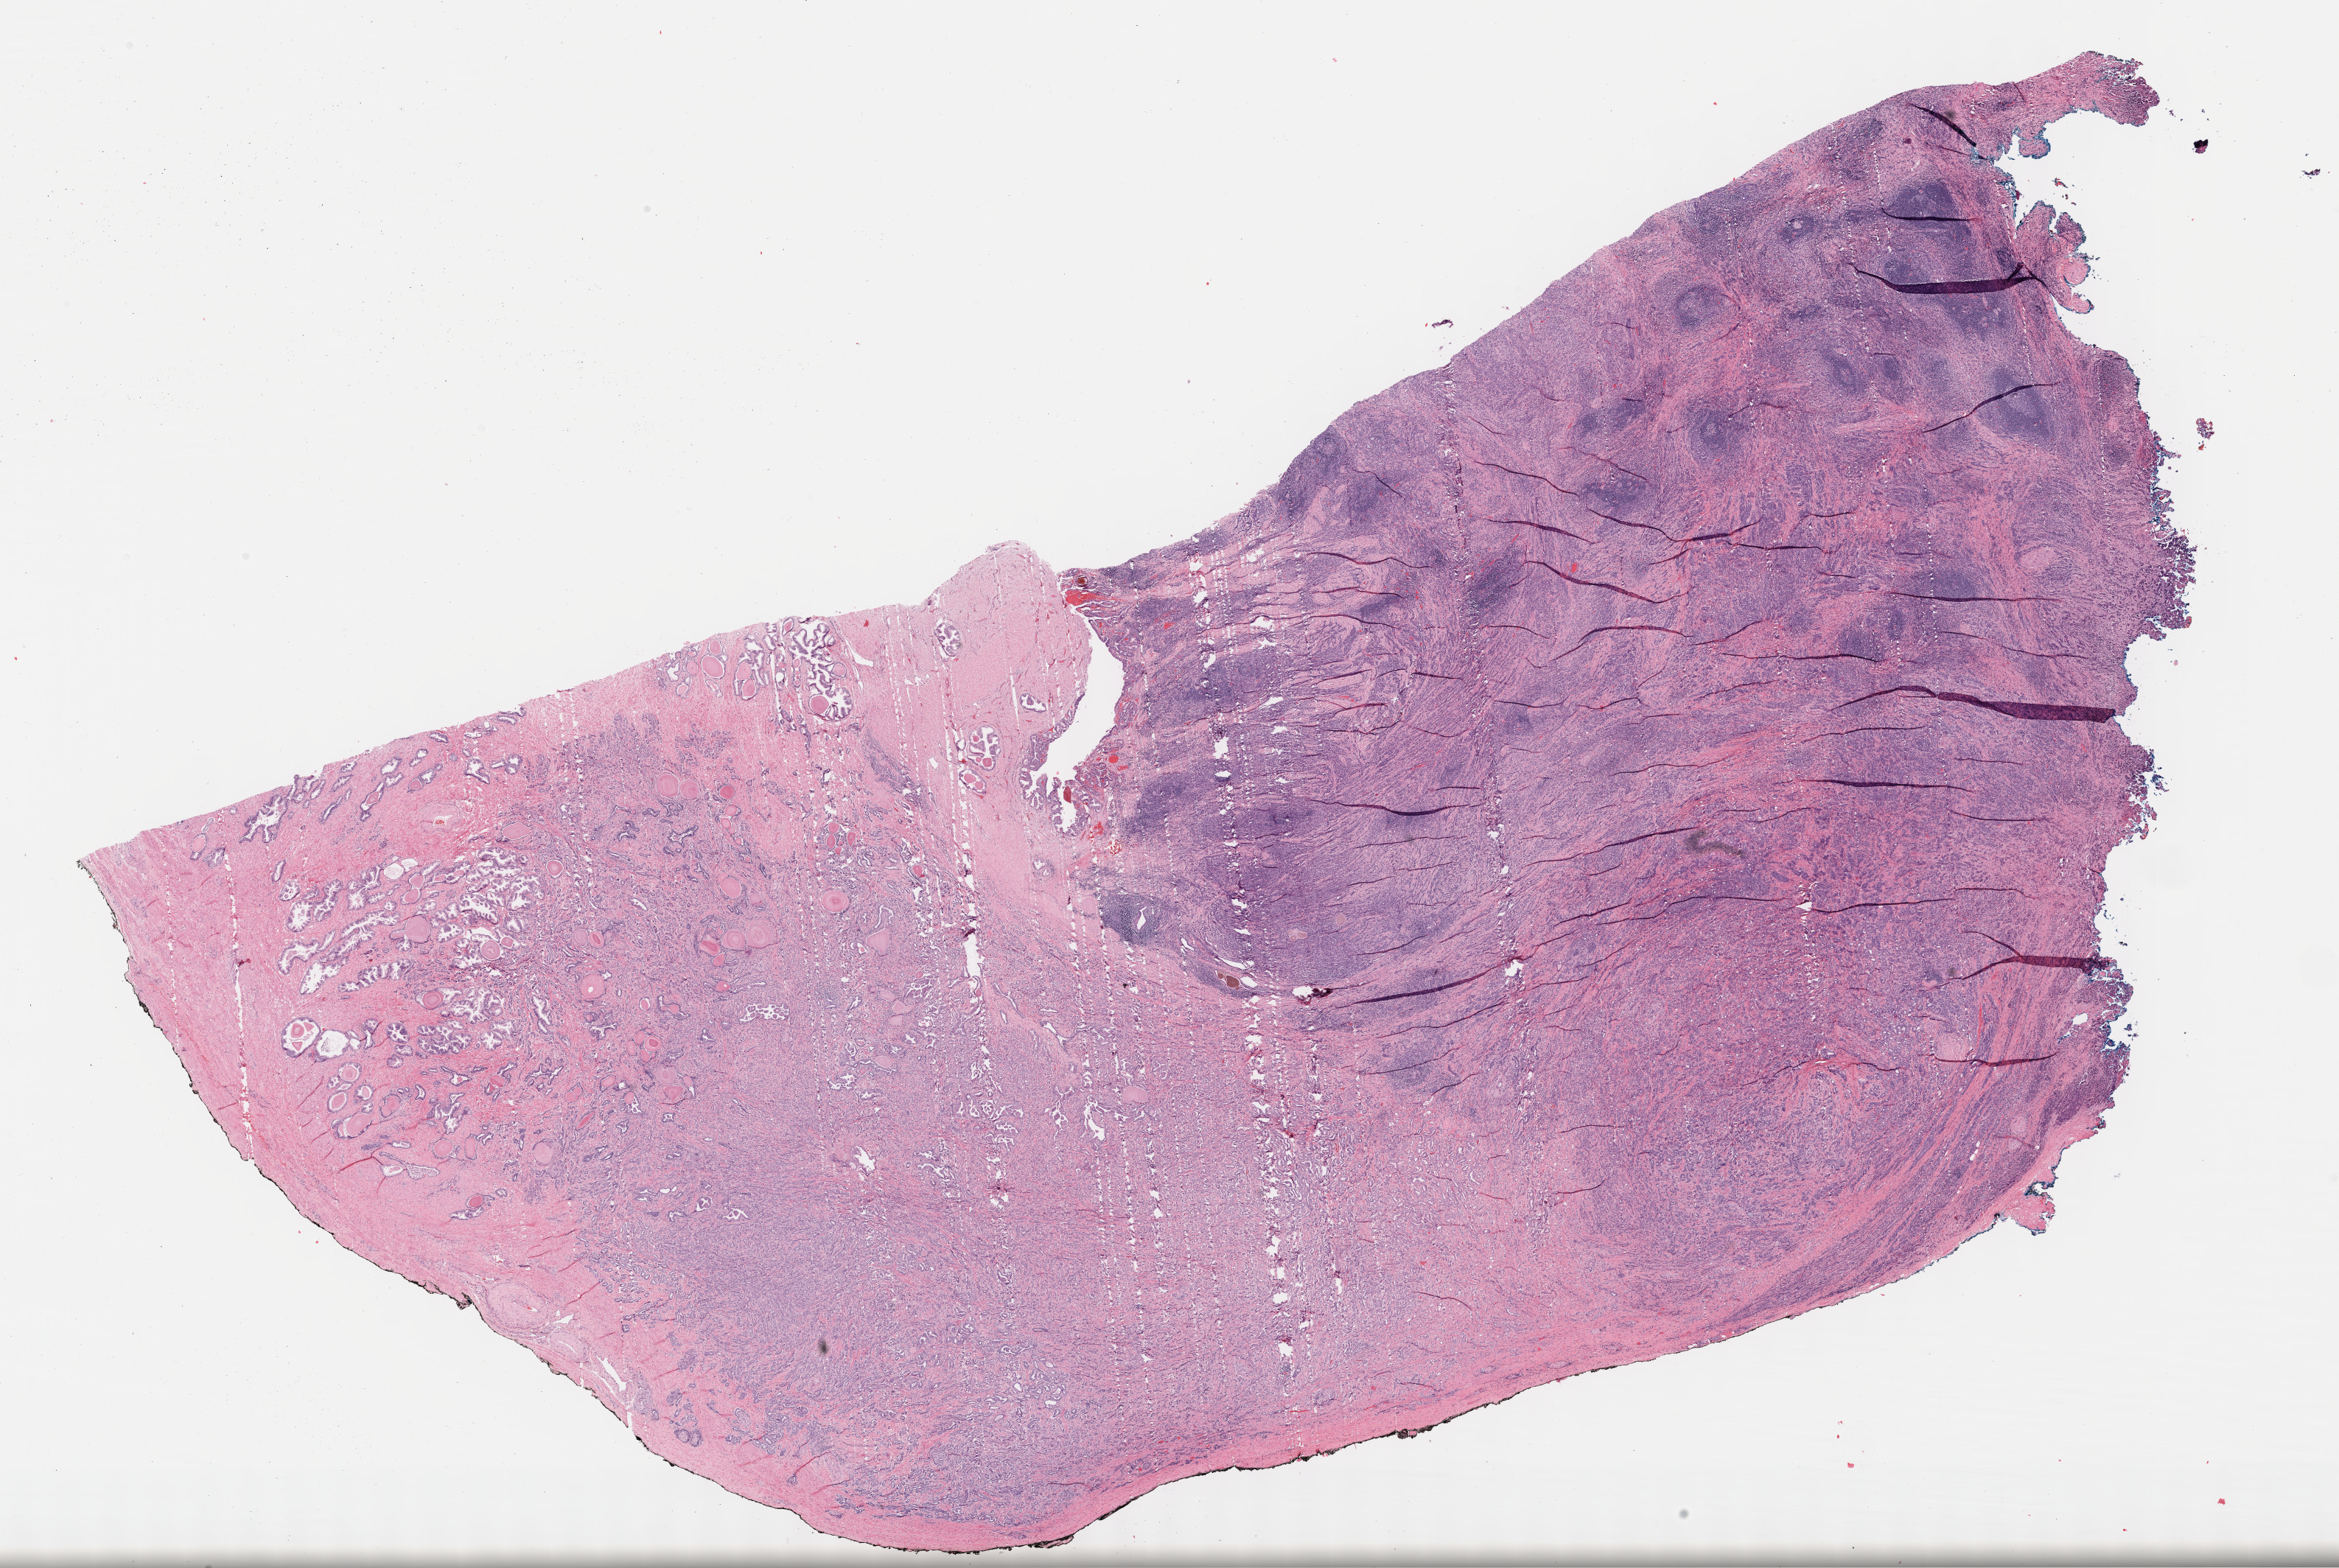
Digitized Hematoxylin and eosin (H&E) stained tissue section (whole slide) — low-resolution overview of the scanned area, about 25.7 x 17.2 mm (from a 40x scan), formalin-fixed paraffin-embedded (FFPE) diagnostic section, primary tumour sample from the prostate. Male, age 57 years at initial diagnosis. Gleason score: 7 (4+3).
- histologic diagnosis: Adenocarcinoma, NOS (prostate gland)
- laterality: bilateral